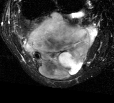
MRI of an extremity soft-tissue mass, one axial slice. Position 21 of 44 along the scan axis. T2-weighted fat-saturated. MR volume resampled by the dataset authors to the PET/CT grid (not the native acquisition matrix). 3.27 mm slice thickness. 114 × 103 image matrix, field of view 111 × 101 mm. Female patient. From the clinical record (not read from this slice): histological type: liposarcoma; site of the primary tumour: right thigh.
Outlined on this slice (expert contour drawn on MRI and transferred to this co-registered scan by the dataset authors):
- gross tumour volume (mass): bounding box (x1, y1, x2, y2) in pixels: (22, 11, 99, 79)